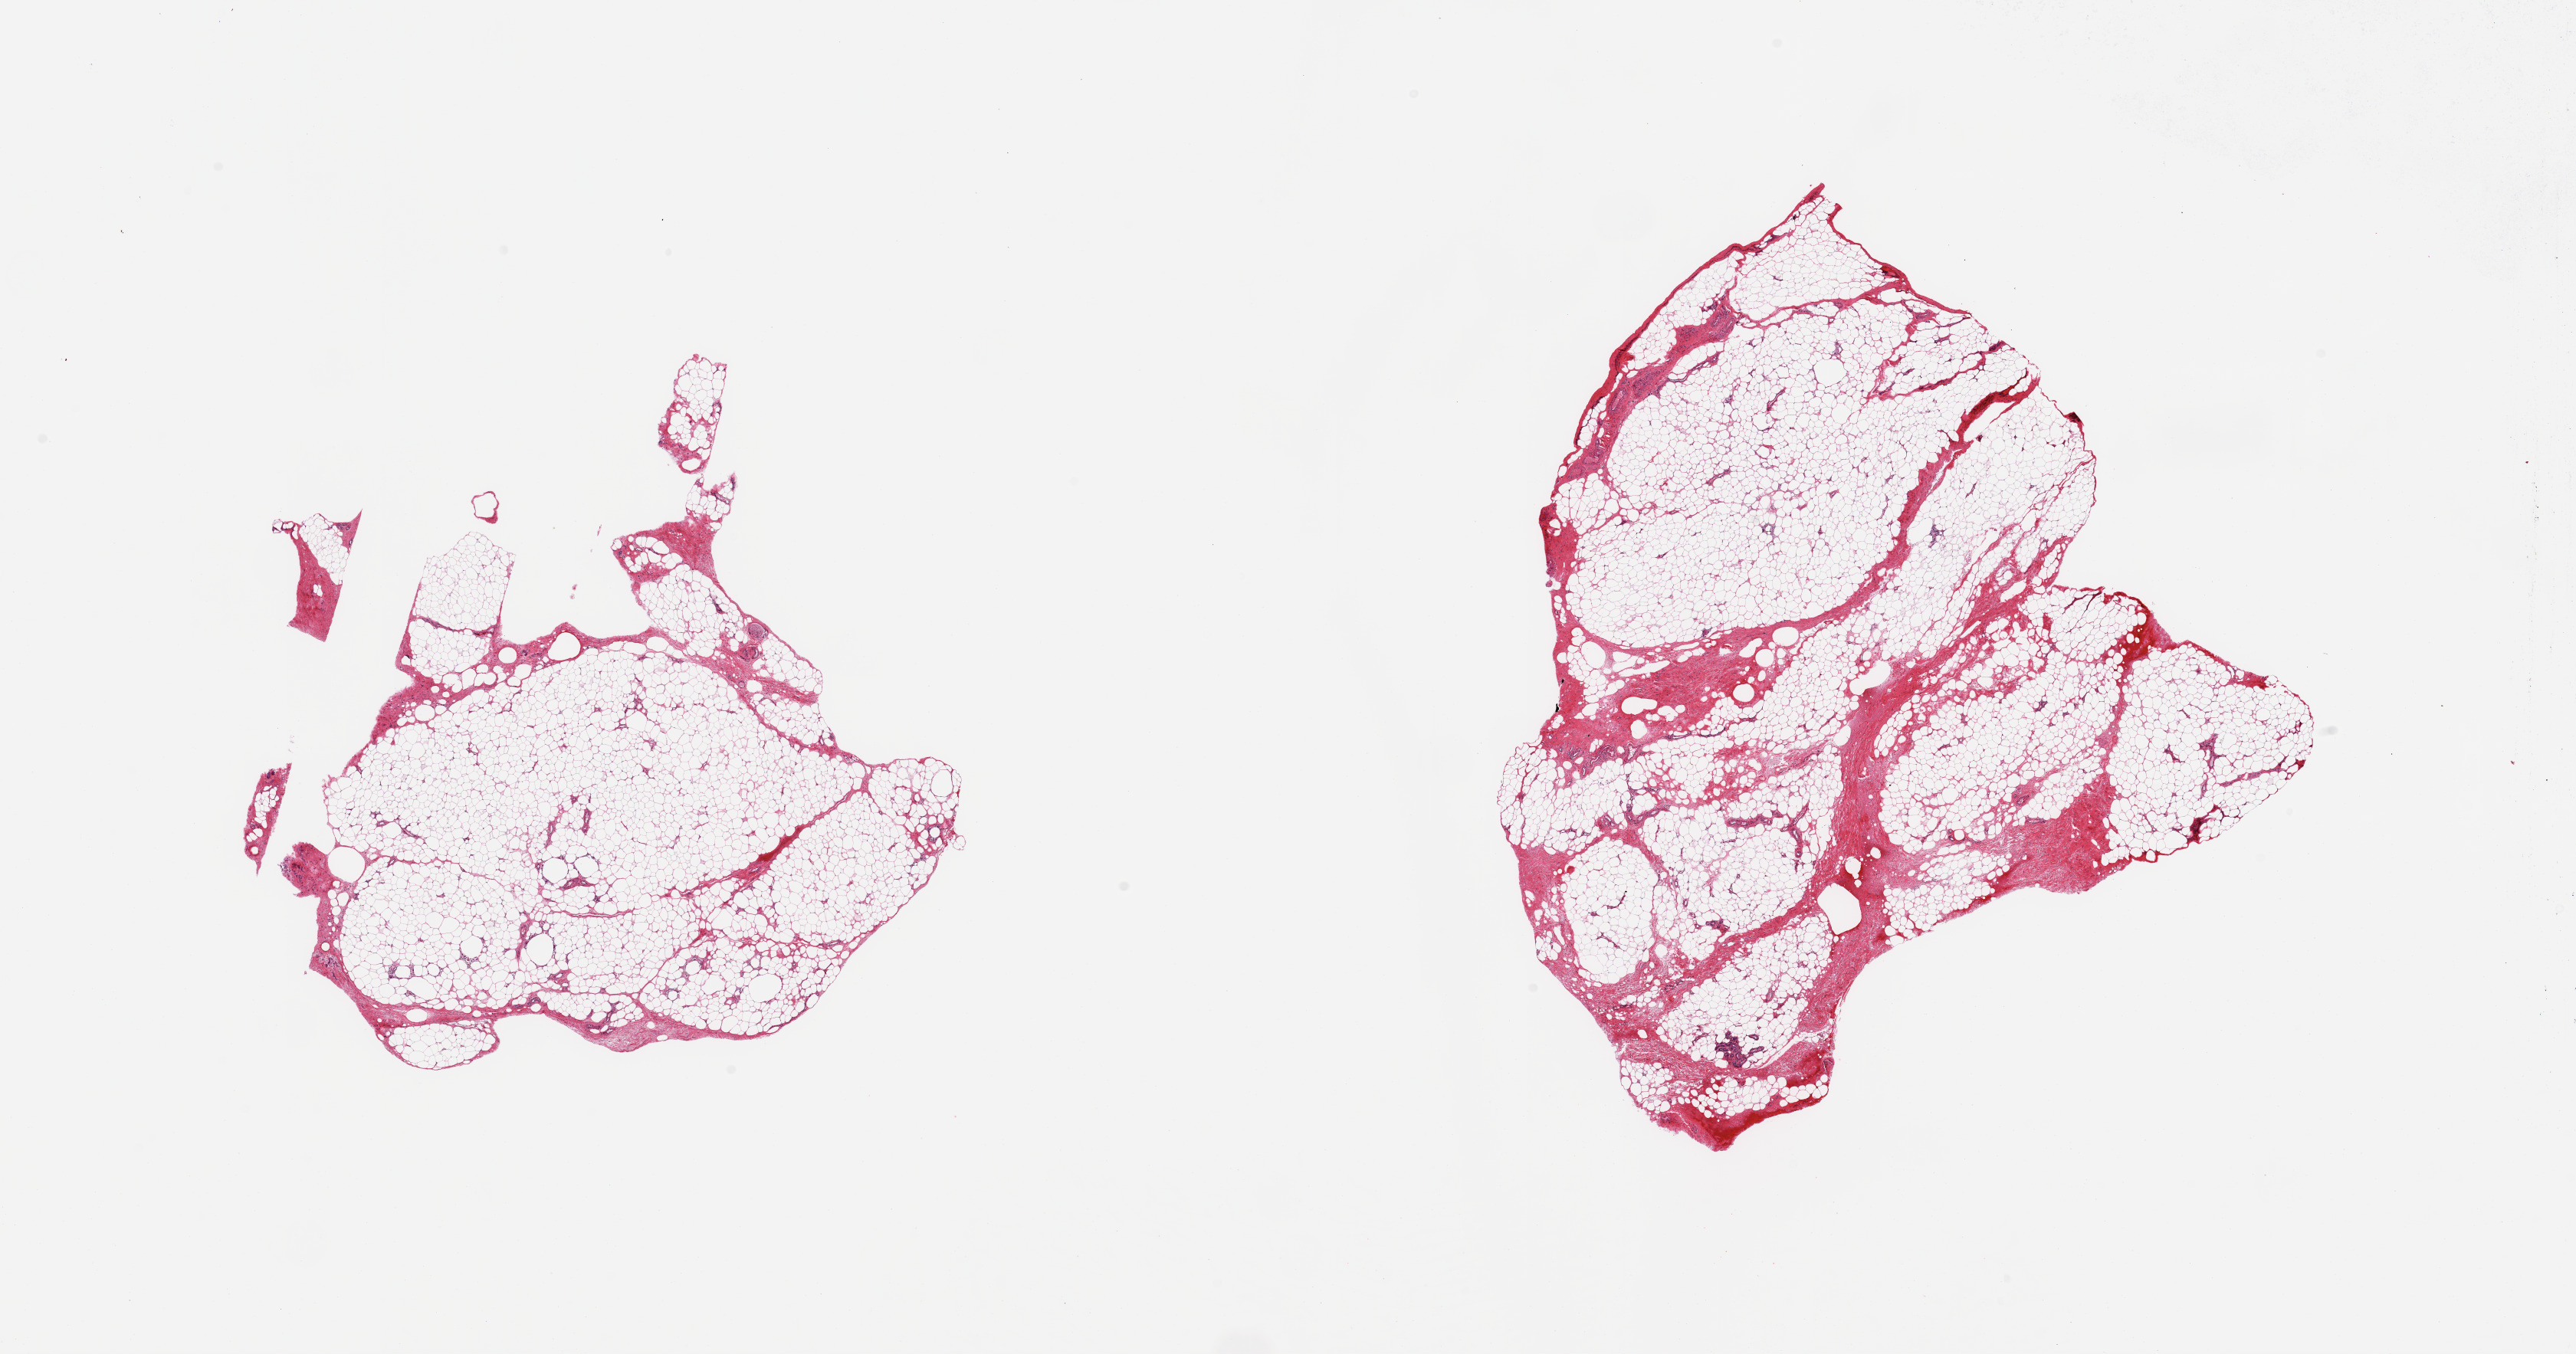
Digitized hematoxylin and eosin (H&E)-stained section — low-resolution overview of the scanned area, about 26.6 x 14.0 mm (acquisition: 20x scan); PAXgene-fixed, paraffin-embedded tissue; section of adipose tissue (target tissue); tissue donor sample.
- review note (as recorded): 2 pieces; 5 & 20% fibrous content